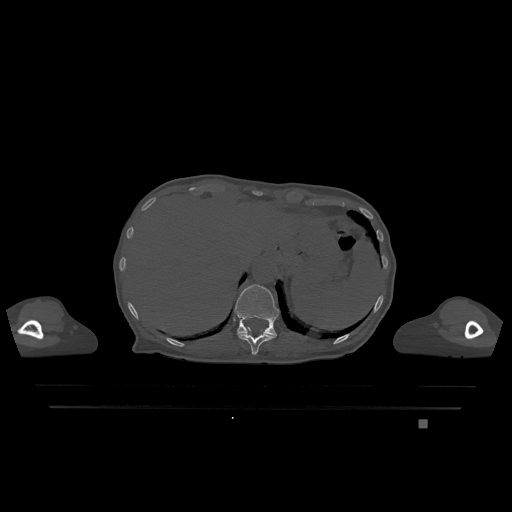
CT including the spine, one axial slice. Slice 561 of 1317 in the series (ordered by position). Bone window (W 1800 / L 400 HU). 0.5 mm slice thickness. 512 × 512 image matrix, field of view 500 × 500 mm. Female patient, age 74 years. From the clinical record (not read from this slice): primary cancer: lung; vertebrae with lytic lesions (as recorded): T1, T4, T5, T6, L4, L5.
Annotated regions visible in this slice (semi-automatically segmented with operator editing):
- T11 vertebra: bounding box [x1, y1, x2, y2] px = [238, 327, 276, 355]
- T12 vertebra: [234, 284, 279, 336]